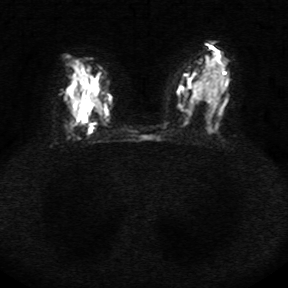
Breast MRI, one axial slice. Slice 16 of 34 in the series (ordered by position). Diffusion-weighted series; image 2 of 4 stored at this slice position (different b-values; order by instance number). 1.5 T. 5 mm slice thickness. 288 × 288 image matrix, field of view 340 × 340 mm. Female patient.
Structures marked on this image (manually delineated by an expert):
- tumour on diffusion-weighted imaging: bounding box (x1, y1, x2, y2) in pixels: (77, 110, 88, 120)